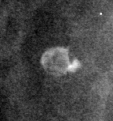
Region of interest cut from a scanned film mammogram (one marked finding), right breast, MLO view.
Finding: calcifications, morphology lucent centered; BI-RADS assessment category 2; benign; no additional work-up was recommended (benign without callback).